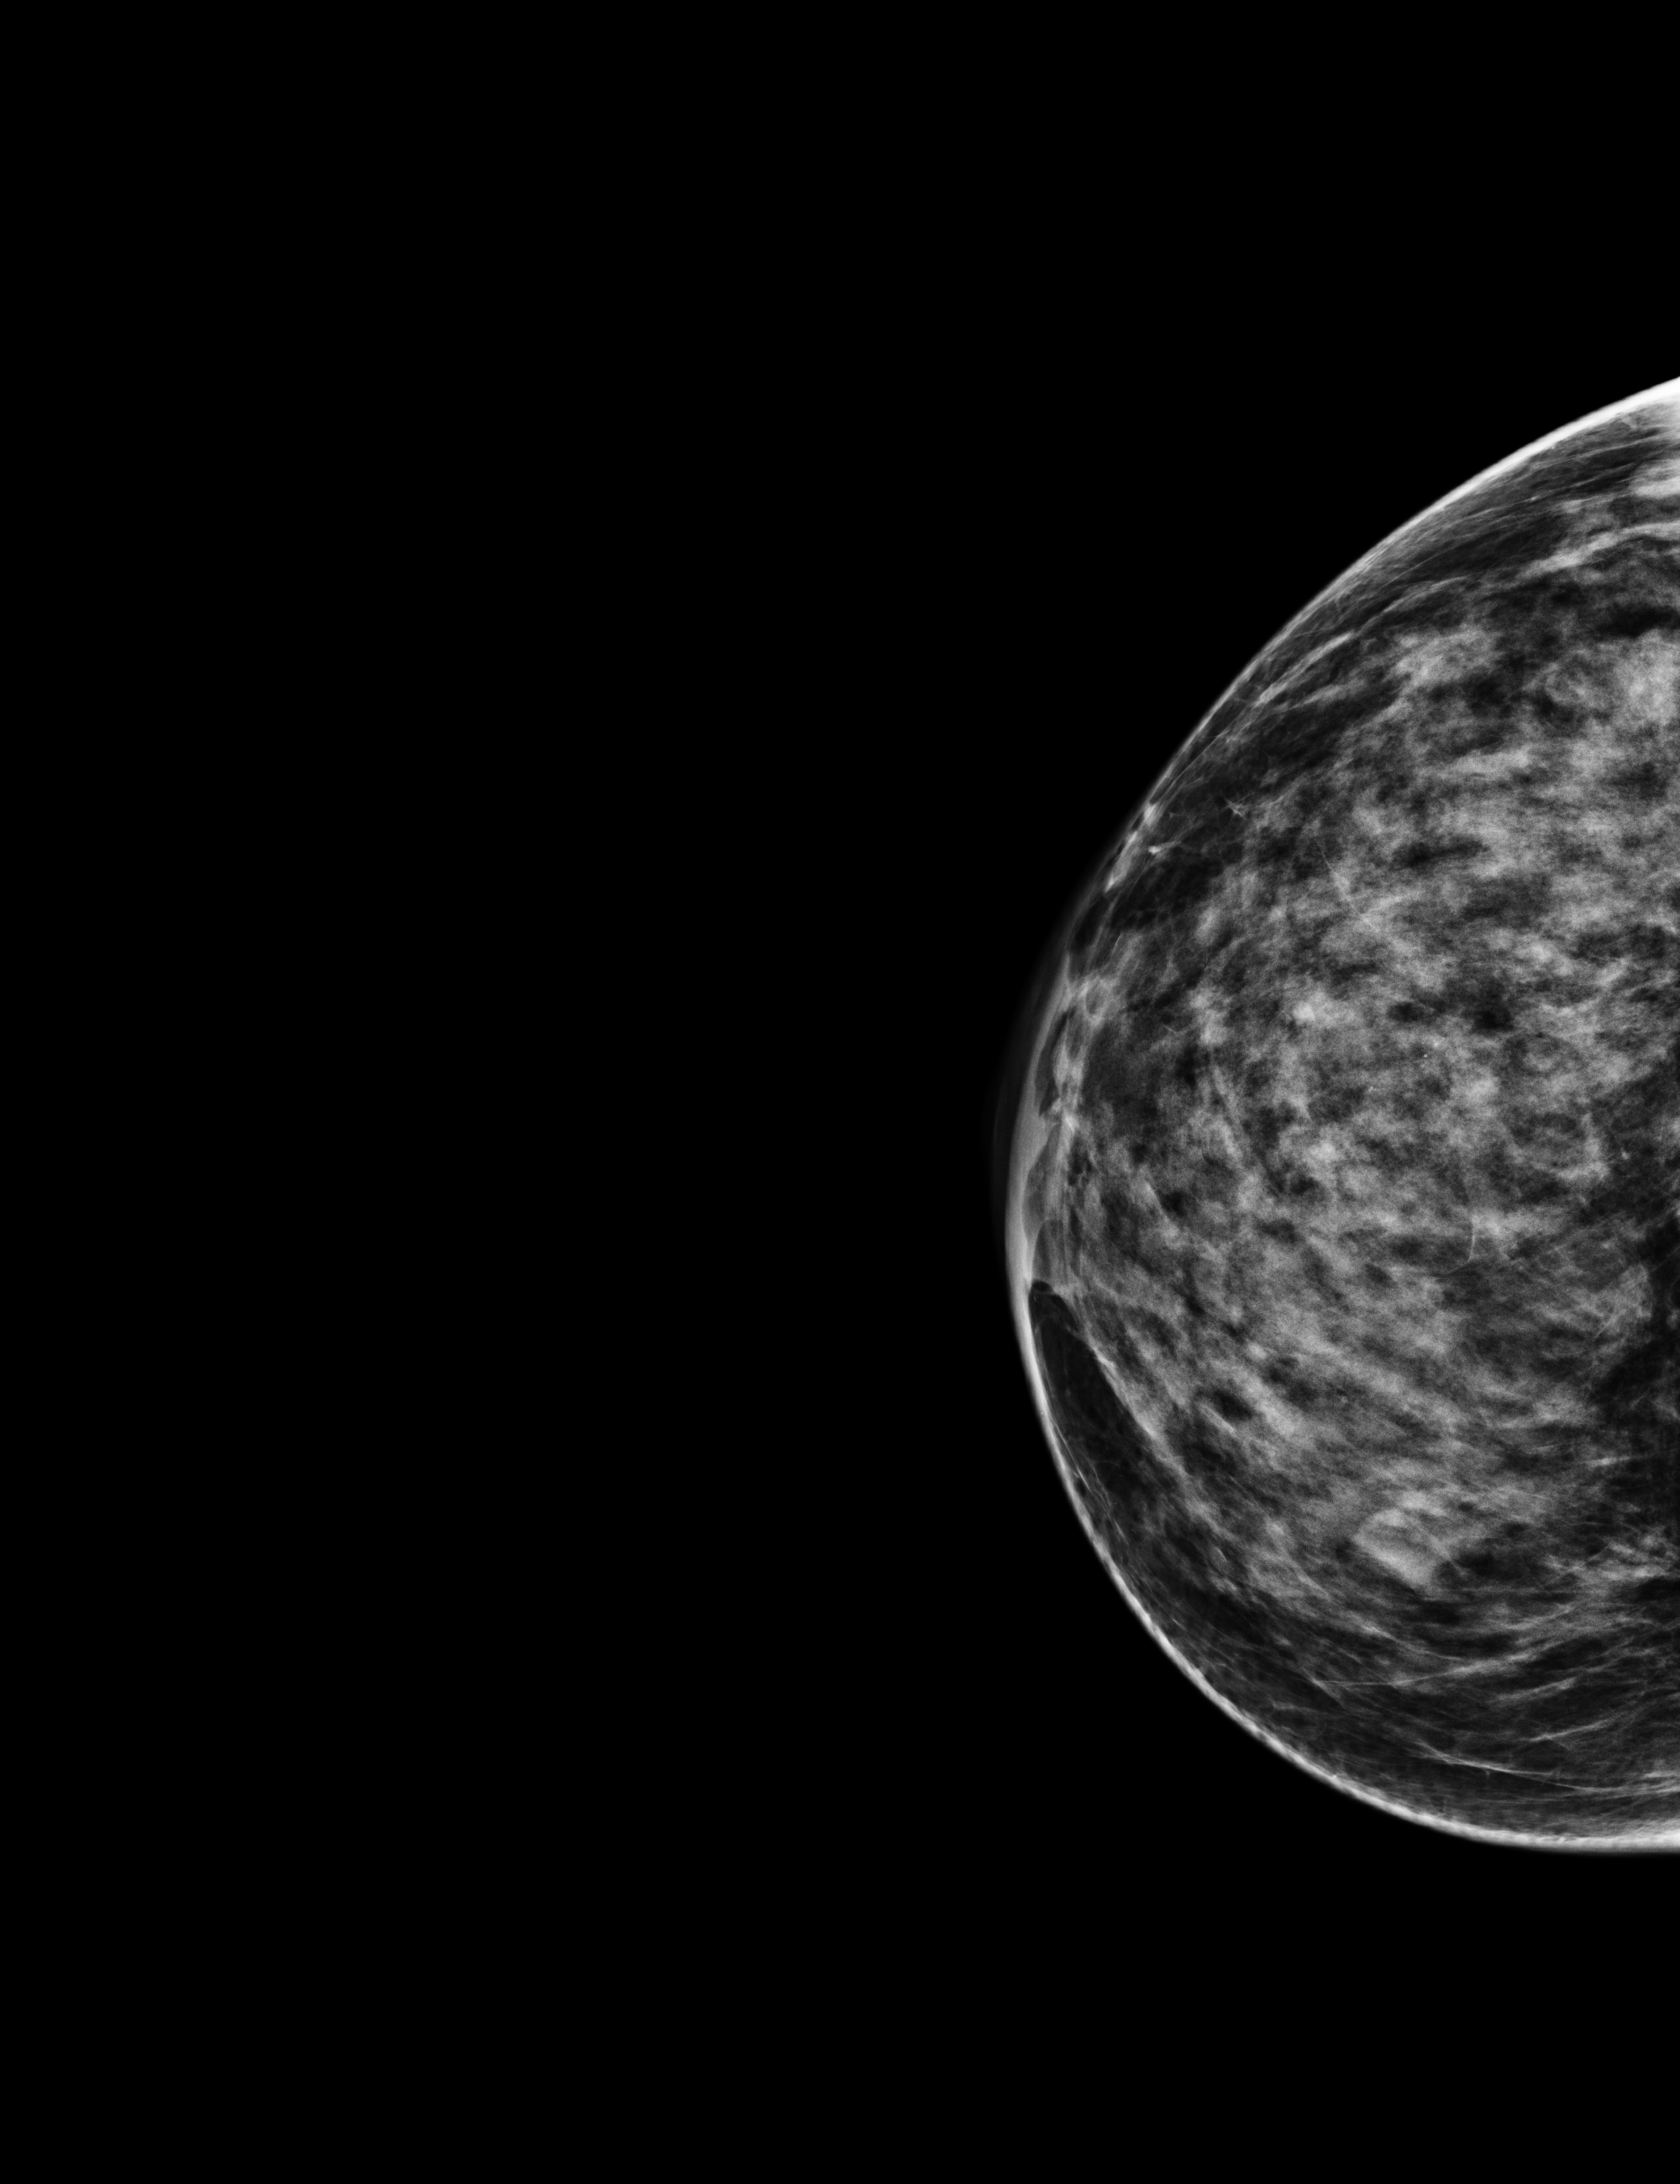
Full-field digital mammogram (FFDM); right breast; CC view; annual screening mammography examination; compressed breast thickness 58 mm. Patient: female, 52 years.
Final BI-RADS assessment for this screening round (tomosynthesis exam, both breasts): category 2.